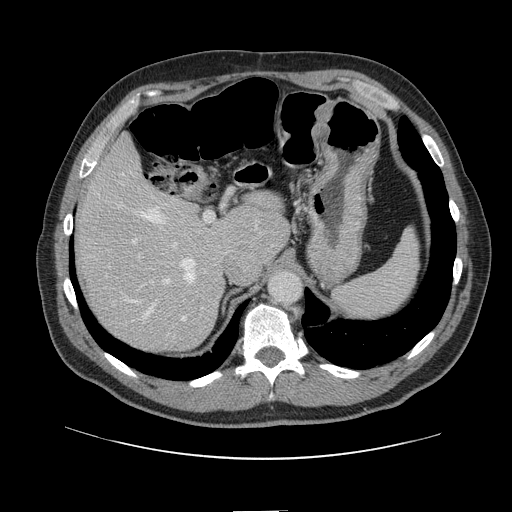
Contrast-enhanced abdominal CT, one axial slice. Position 98 of 161 along the scan axis. 120 kVp. Intravenous contrast given. Soft-tissue window (W 400 / L 40 HU). 512 × 512 image matrix. Male patient, age 66 years. Case-level facts recorded for this patient, not image findings: diagnosis: colorectal cancer liver metastases, imaged before liver resection; multiple liver metastases: no; largest metastasis: 3.5 cm; disease in both lobes: no.
Annotated regions visible in this slice (expert manual segmentation):
- hepatic veins: bounding box <119,174,195,318> (left, top, right, bottom; pixels)
- liver: <81,142,286,351>
- planned liver remnant (the part of the liver to remain after resection): <81,141,286,306>
- portal vein (with intrahepatic branches): <131,212,216,311>